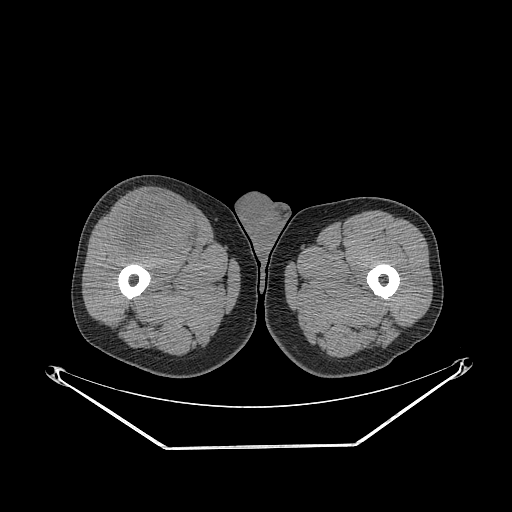
CT of an extremity soft-tissue mass (from a PET/CT study), one axial slice; position 278 of 311 along the scan axis; 140 kVp; soft-tissue window (W 400 / L 40 HU); 3.75 mm slice thickness; 512 × 512 image matrix. Male patient. Case-level facts recorded for this patient, not image findings: histological type: pleiomorphic leiomyosarcoma; grade: intermediate; site of the primary tumour: right thigh.
Outlined on this slice (expert contour drawn on MRI and transferred to this co-registered scan by the dataset authors):
- gross tumour volume including surrounding oedema: box from (x=112, y=194) to (x=200, y=257) px
- gross tumour volume (mass): (x=112, y=194)–(x=200, y=257)